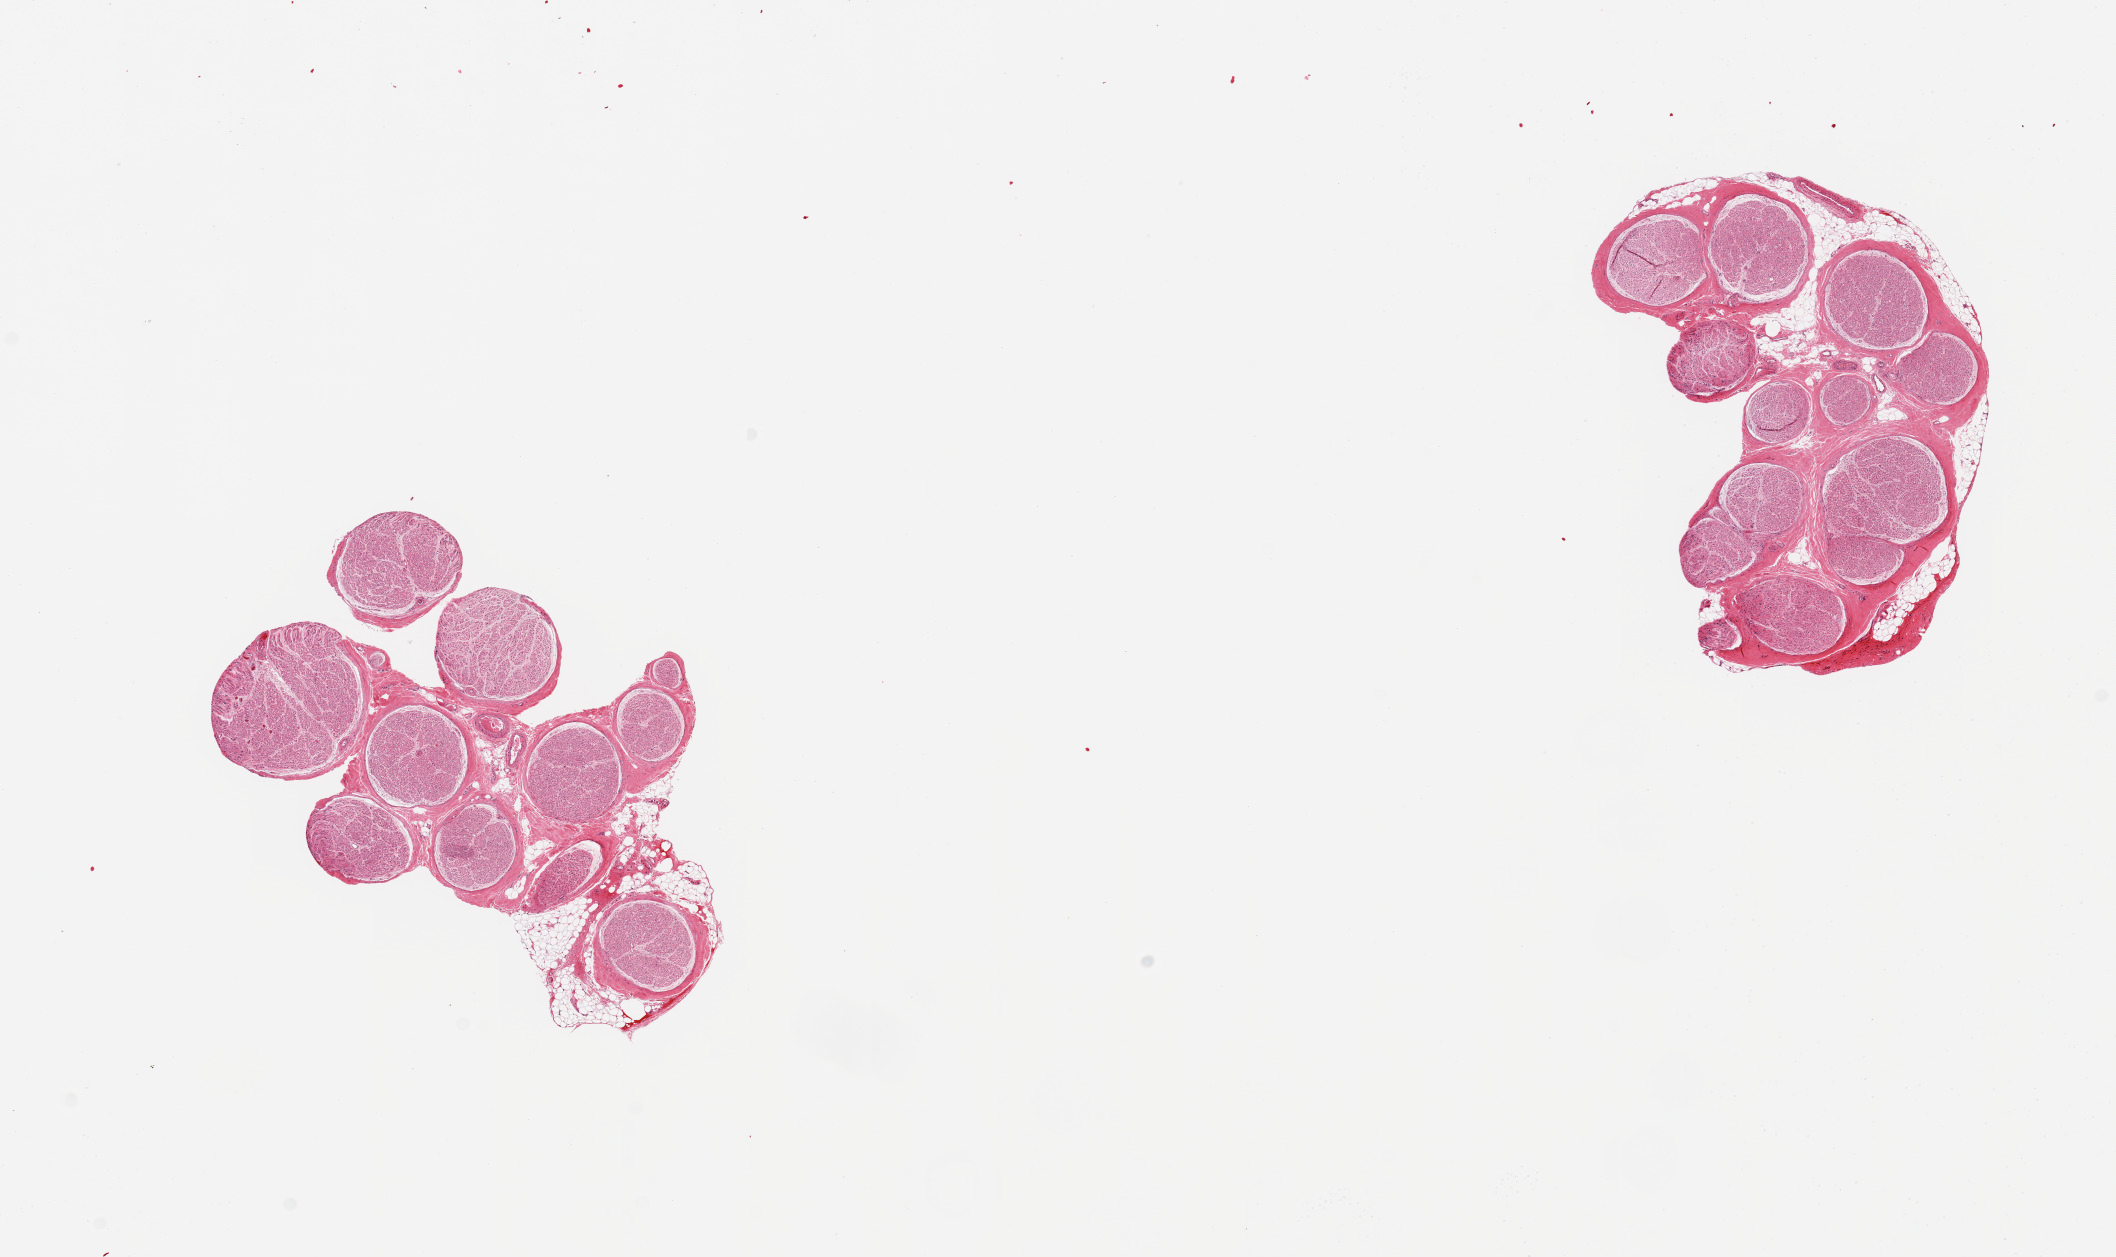
Whole-slide image, hematoxylin and eosin (H&E) stain, brightfield, low-resolution overview of the scanned area, about 16.7 x 9.9 mm, PAXgene-fixed paraffin-embedded (PFPE) section, target tissue: tibial nerve, donor tissue sample. Male donor.
Pathologist's review note for this sample: 2 pieces, generally clean specimens, focal adherent fat, up to ~0.5mm.